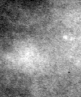
Cropped region of a digitized screen-film mammogram centred on a radiologist-marked abnormality, left breast, MLO view.
- Marked abnormality: calcifications, morphology amorphous / round and regular, distribution clustered; BI-RADS assessment category 4; pathology result (as recorded, not read from the image): malignant.